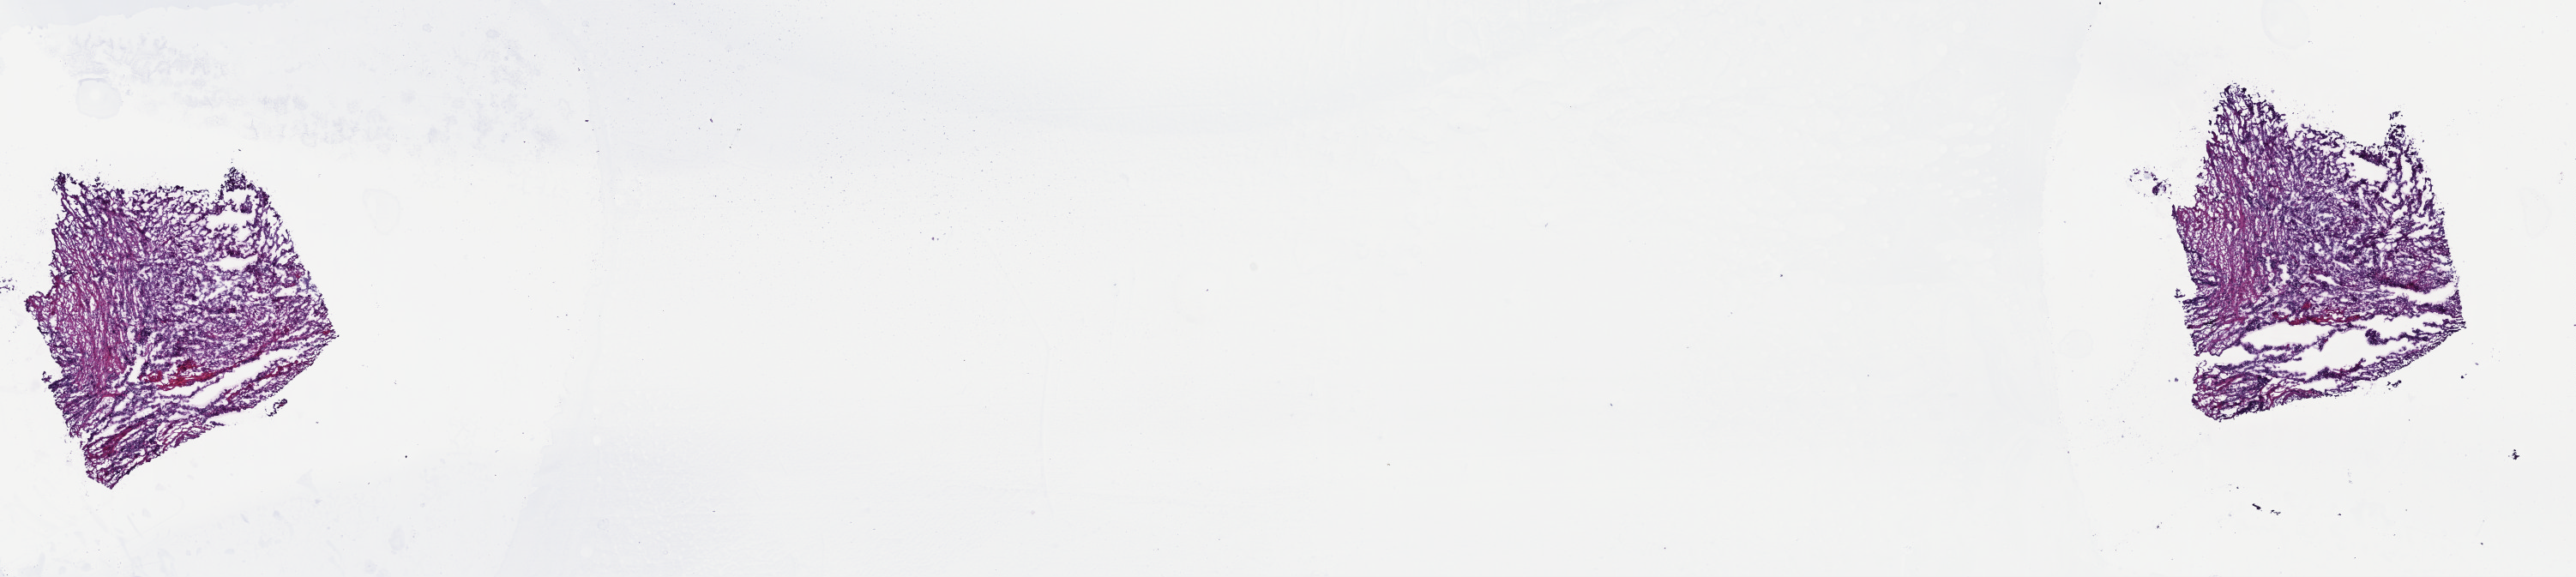
Digitized Hematoxylin and eosin (H&E) stained tissue section (whole slide), shown as a low-resolution overview of the whole scanned area (about 23.6 x 5.3 mm, from a 40x scan), frozen section from the top of the tissue portion, sample: primary tumour, head and neck. Male, age 68 years at initial diagnosis. Histologic grade: G2 (moderately differentiated). Composition of this section per pathologist review: tumour cells 78%, tumour nuclei 85%, normal cells 0%, stromal cells 10%, necrosis 12%. Infiltration values recorded for this section: lymphocyte infiltration 10%, monocyte infiltration 0%, neutrophil infiltration 0%.
• pathologic diagnosis: Squamous cell carcinoma, NOS (mouth, NOS)
• AJCC pathologic stage: II